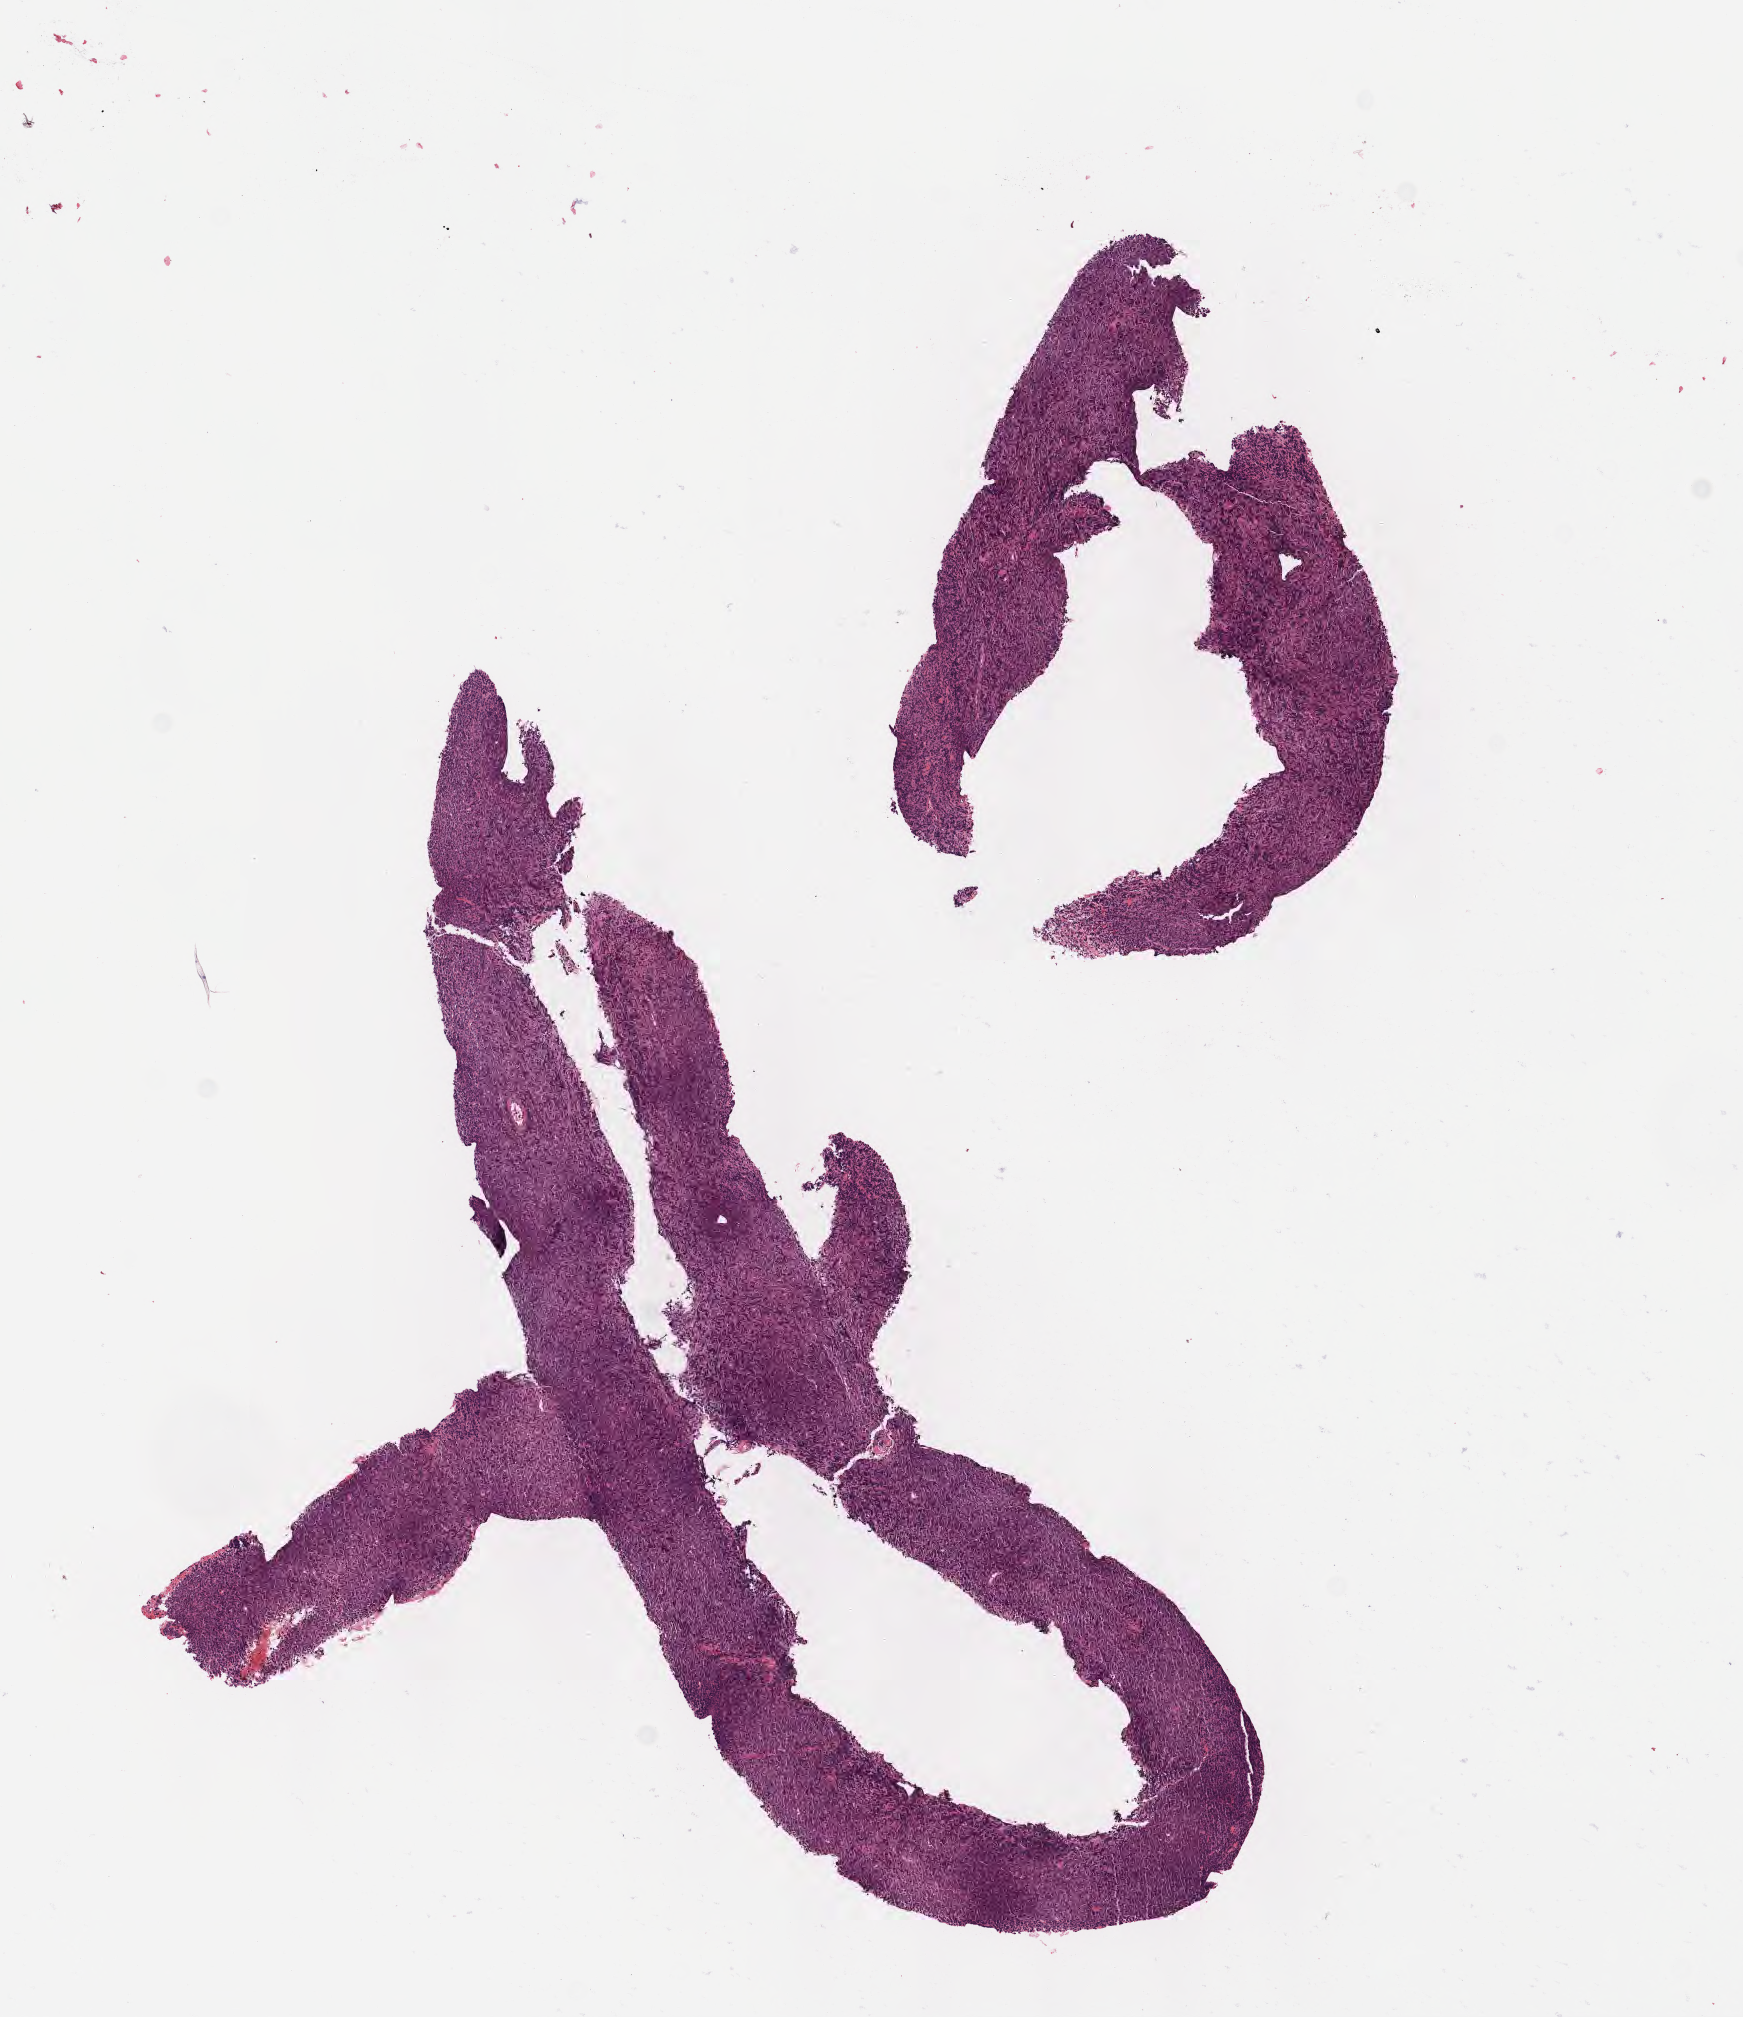
Whole-slide image, H&E stain, a low-resolution overview of the entire scanned area, about 7.0 x 8.1 mm. Patient male; aged 52.
Specimen: tumor tissue; anatomic site: liver.